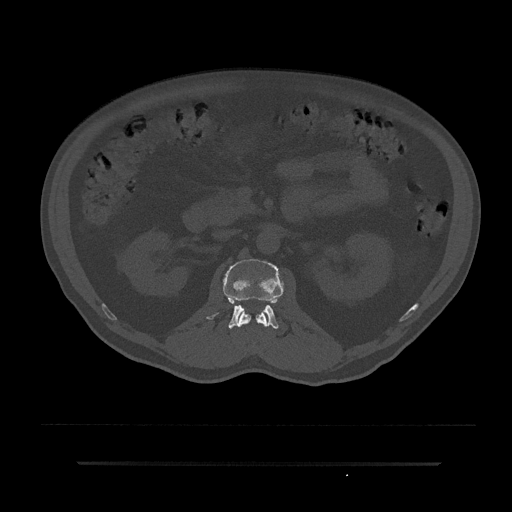
CT including the spine, one axial slice. Slice 103 of 797 in the series (ordered by position). Reconstruction kernel Br40s/3. 120 kVp. Bone window (W 1800 / L 400 HU). 512 × 512 image matrix, field of view 464 × 464 mm. Patient: male, 59 years. From the clinical record (not read from this slice): primary cancer: bile ducts; vertebrae with lytic lesions (as recorded): T10.
Structures marked on this image (semi-automatically segmented with operator editing):
- L1 vertebra: box from (x=238, y=310) to (x=268, y=327) px
- L2 vertebra: (x=207, y=259)–(x=283, y=329)